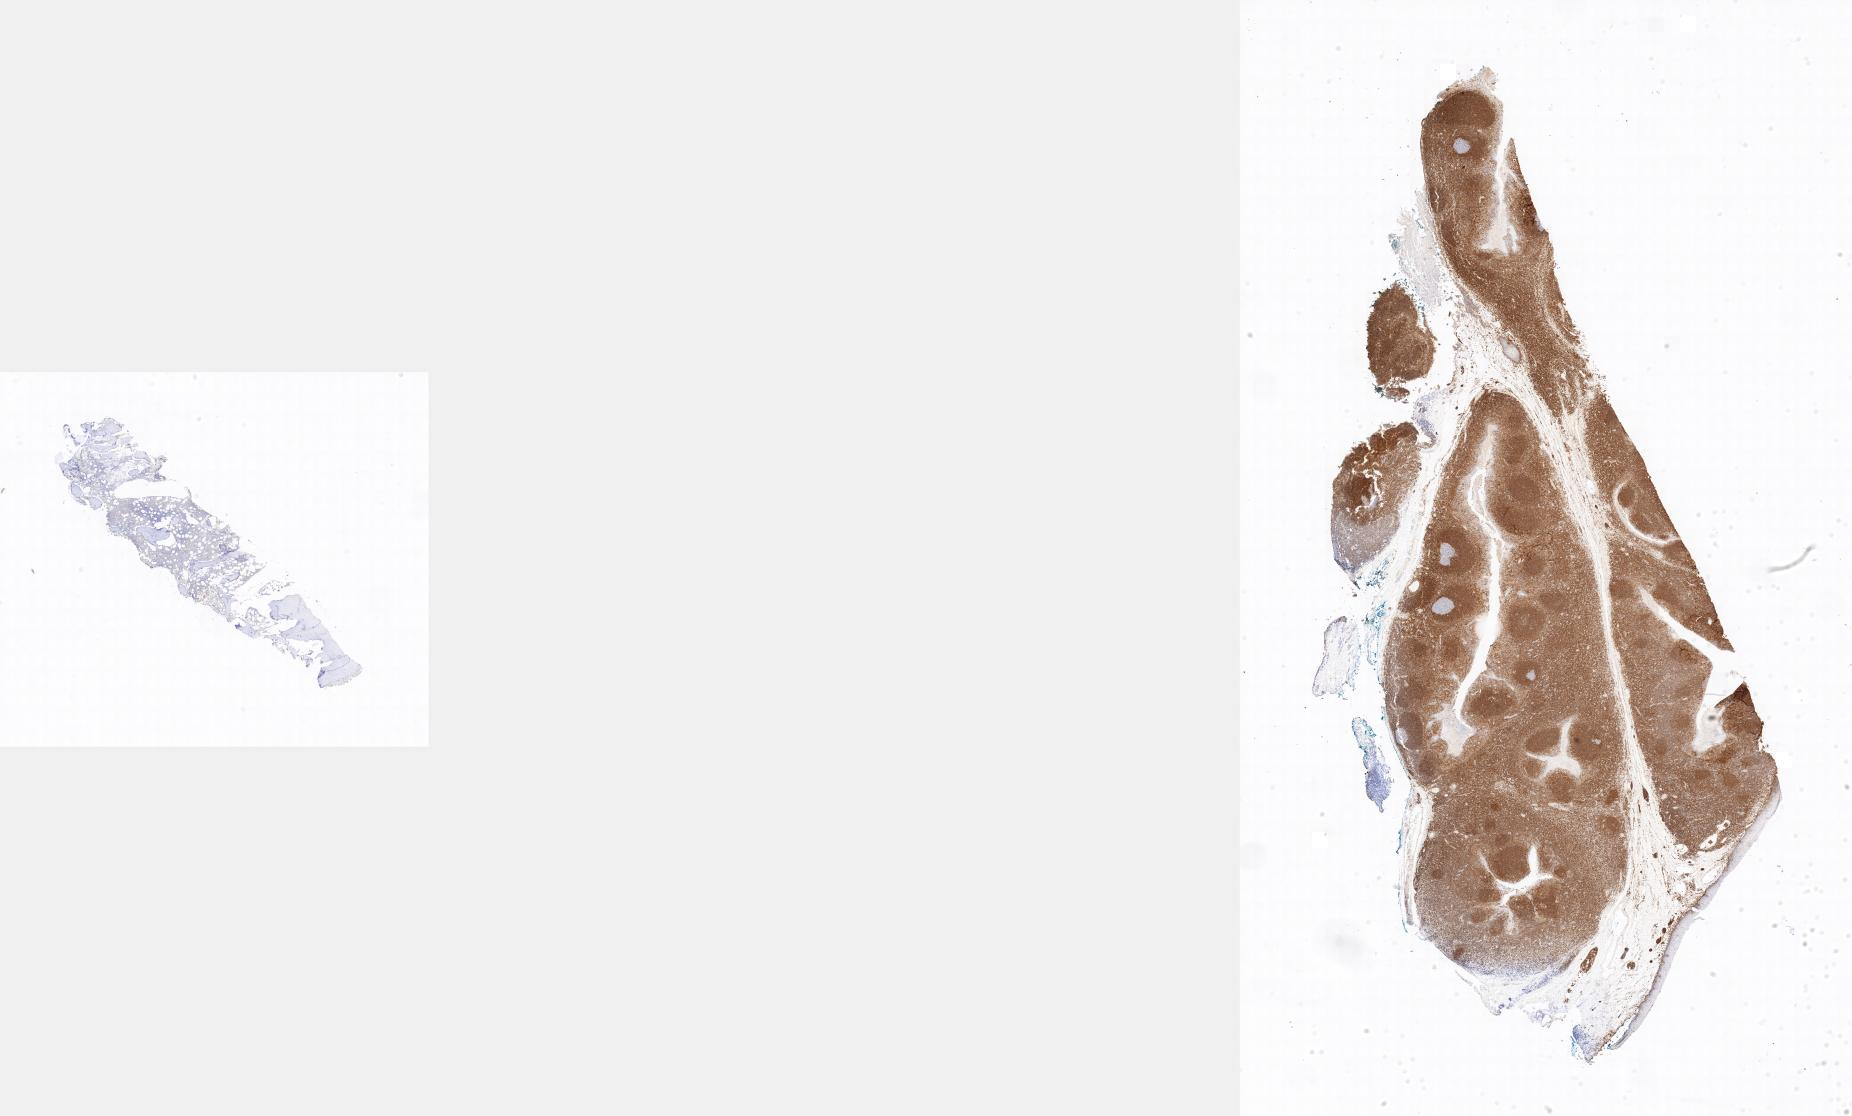
Immunohistochemistry (IHC) whole-slide image stained for BCL2 — a low-resolution overview of the entire scanned area; tumor tissue; anatomic site: bone marrow. Female patient; age at initial diagnosis 4 years.
Histologic diagnosis: Burkitt lymphoma, NOS.